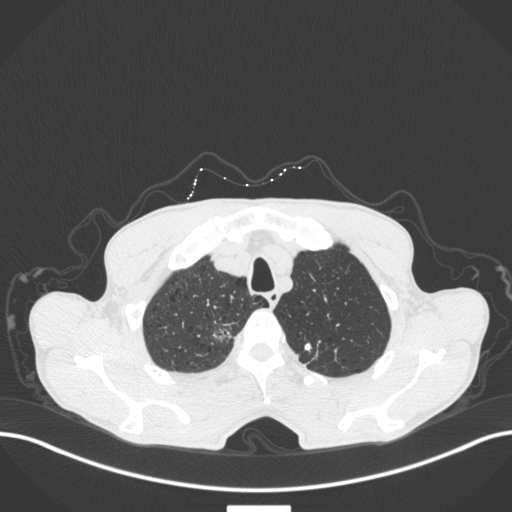
Chest CT, one axial slice. Slice 373 of 445 in the series (ordered by position). Reconstruction kernel B31f. Lung window (W 1500 / L -600 HU). 1 mm slice thickness. 512 × 512 image matrix. Patient: male, 70 years. Case-level facts recorded for this patient, not image findings: clinical TNM (as recorded): T1a N0 M0; histopathological grade: G1-2.
Structures marked on this image (bounding box drawn by a radiologist):
- lung tumour (recorded histology: adenocarcinoma): box from (x=208, y=318) to (x=237, y=345) px